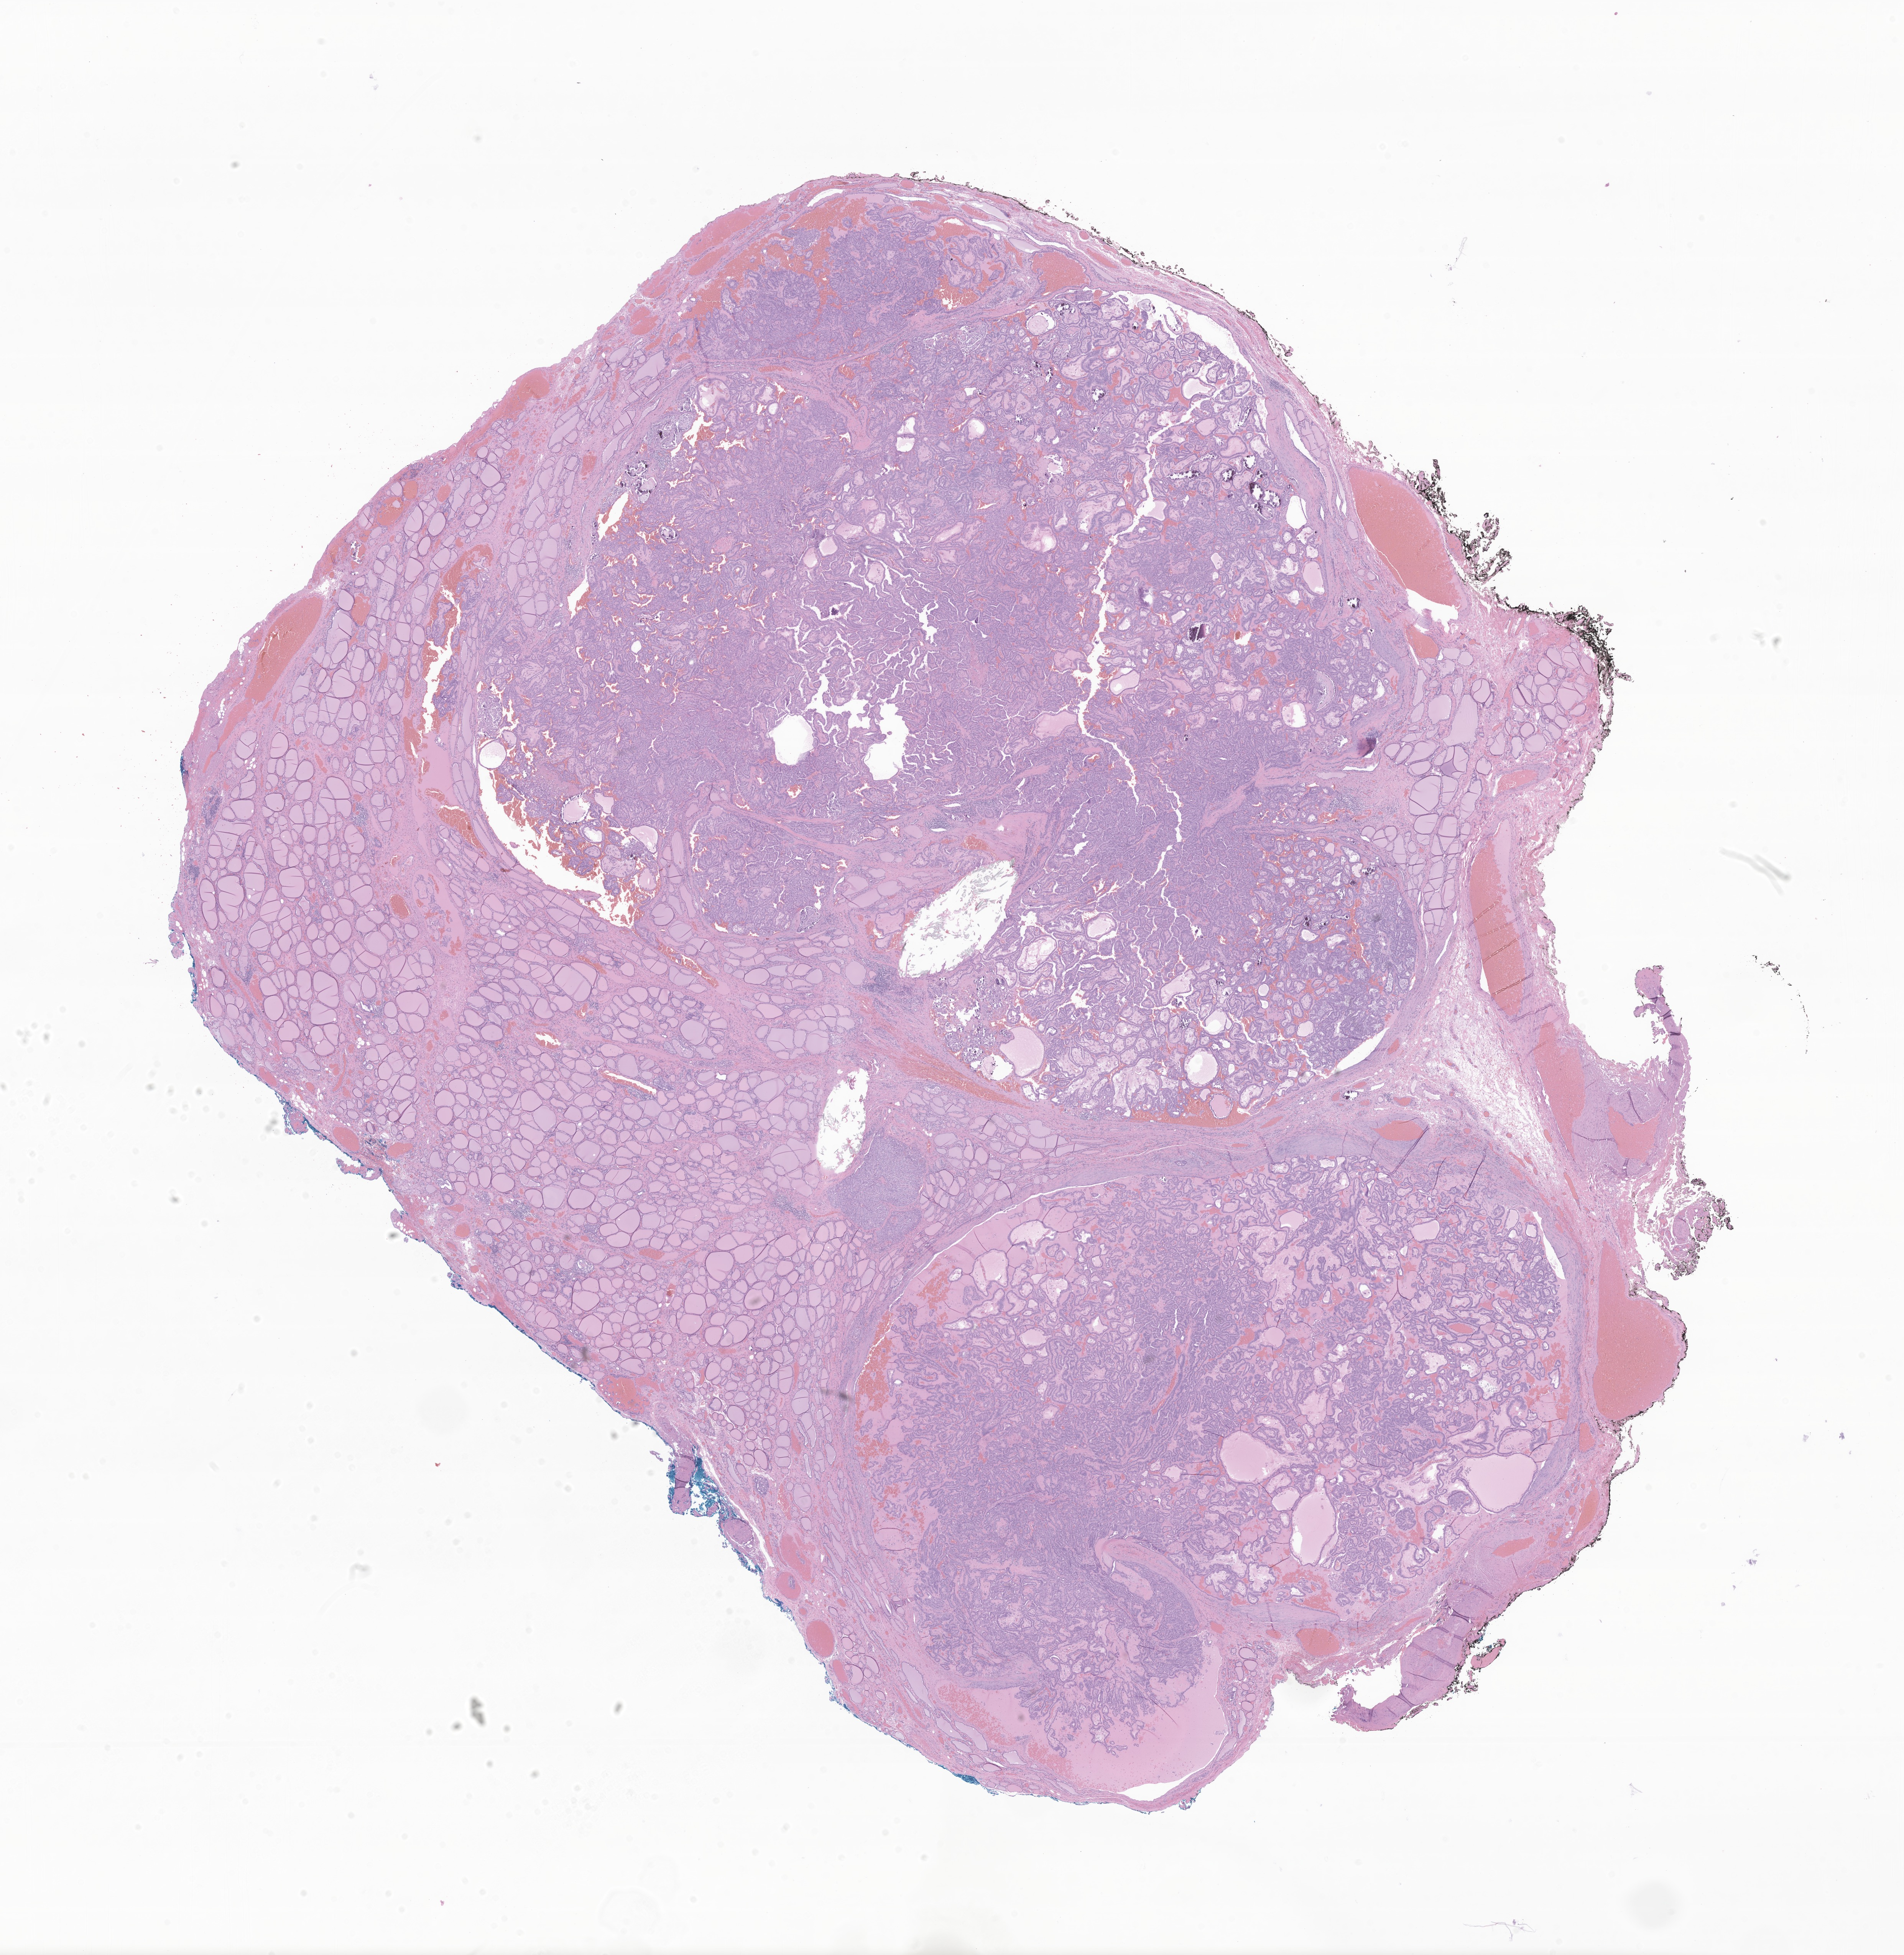
Haematoxylin and eosin whole-slide image of tumor tissue from the thyroid — whole scanned area (about 20.9 x 21.5 mm) shown as a low-resolution overview. Formalin-fixed, paraffin-embedded (FFPE) tissue. Patient: female, age 200 months (16 years 8 months).
Recorded diagnosis: Papillary carcinoma, NOS.